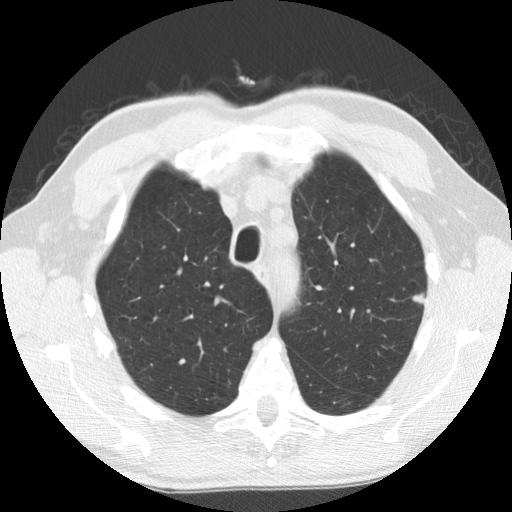
Low-dose screening chest CT, axial slice; third annual screen; lung window (W 1500 / L -600 HU); 2.5 mm slice thickness; standard (soft-tissue) reconstruction kernel (STANDARD); 120 kVp; slice 29 of 158 in the series. Male, age 63 years at enrolment. Current smoker at enrolment.
Expert-annotated lung lesion, bounding box <400,279,438,313> (left, top, right, bottom; pixels). Screening reader's record for this exam (one nodule recorded; not confirmed to be the boxed lesion): non-calcified nodule or mass ≥4 mm, left upper lobe, 8 × 6 mm, smooth margins, ground glass attenuation, pre-existing on the prior screen: yes; interval growth: yes. Official screen result: positive, other.